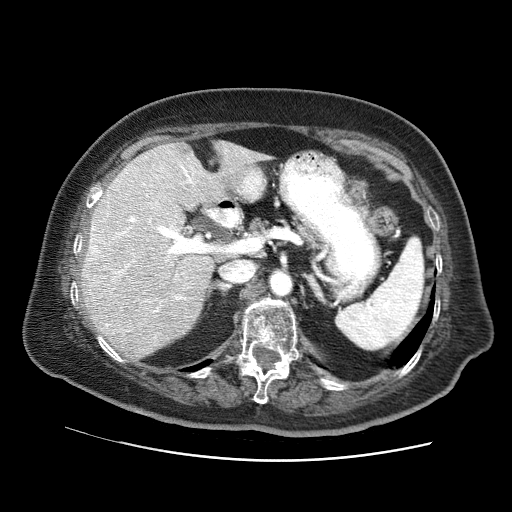
Contrast-enhanced abdominal CT (liver protocol), one axial slice; reconstruction kernel STANDARD; 120 kVp; soft-tissue window (W 400 / L 40 HU); 512 × 512 image matrix, field of view 380 × 380 mm. Case-level facts recorded for this patient, not image findings: diagnosis: hepatocellular carcinoma (patient treated with transarterial chemoembolisation; whether this scan precedes or follows treatment is not stated here); TNM stage (as recorded): Stage-I; Child-Pugh class: A; tumour differentiation: well differentiated; tumour nodularity: uninodular.
Annotated regions visible in this slice (semi-automatically segmented with operator editing):
- liver parenchyma outside the tumour (the mass and vessels are separate outlines, so this box may not span the whole liver): bounding box (x1, y1, x2, y2) in pixels: (82, 140, 267, 356)
- liver vessels: (90, 165, 261, 326)